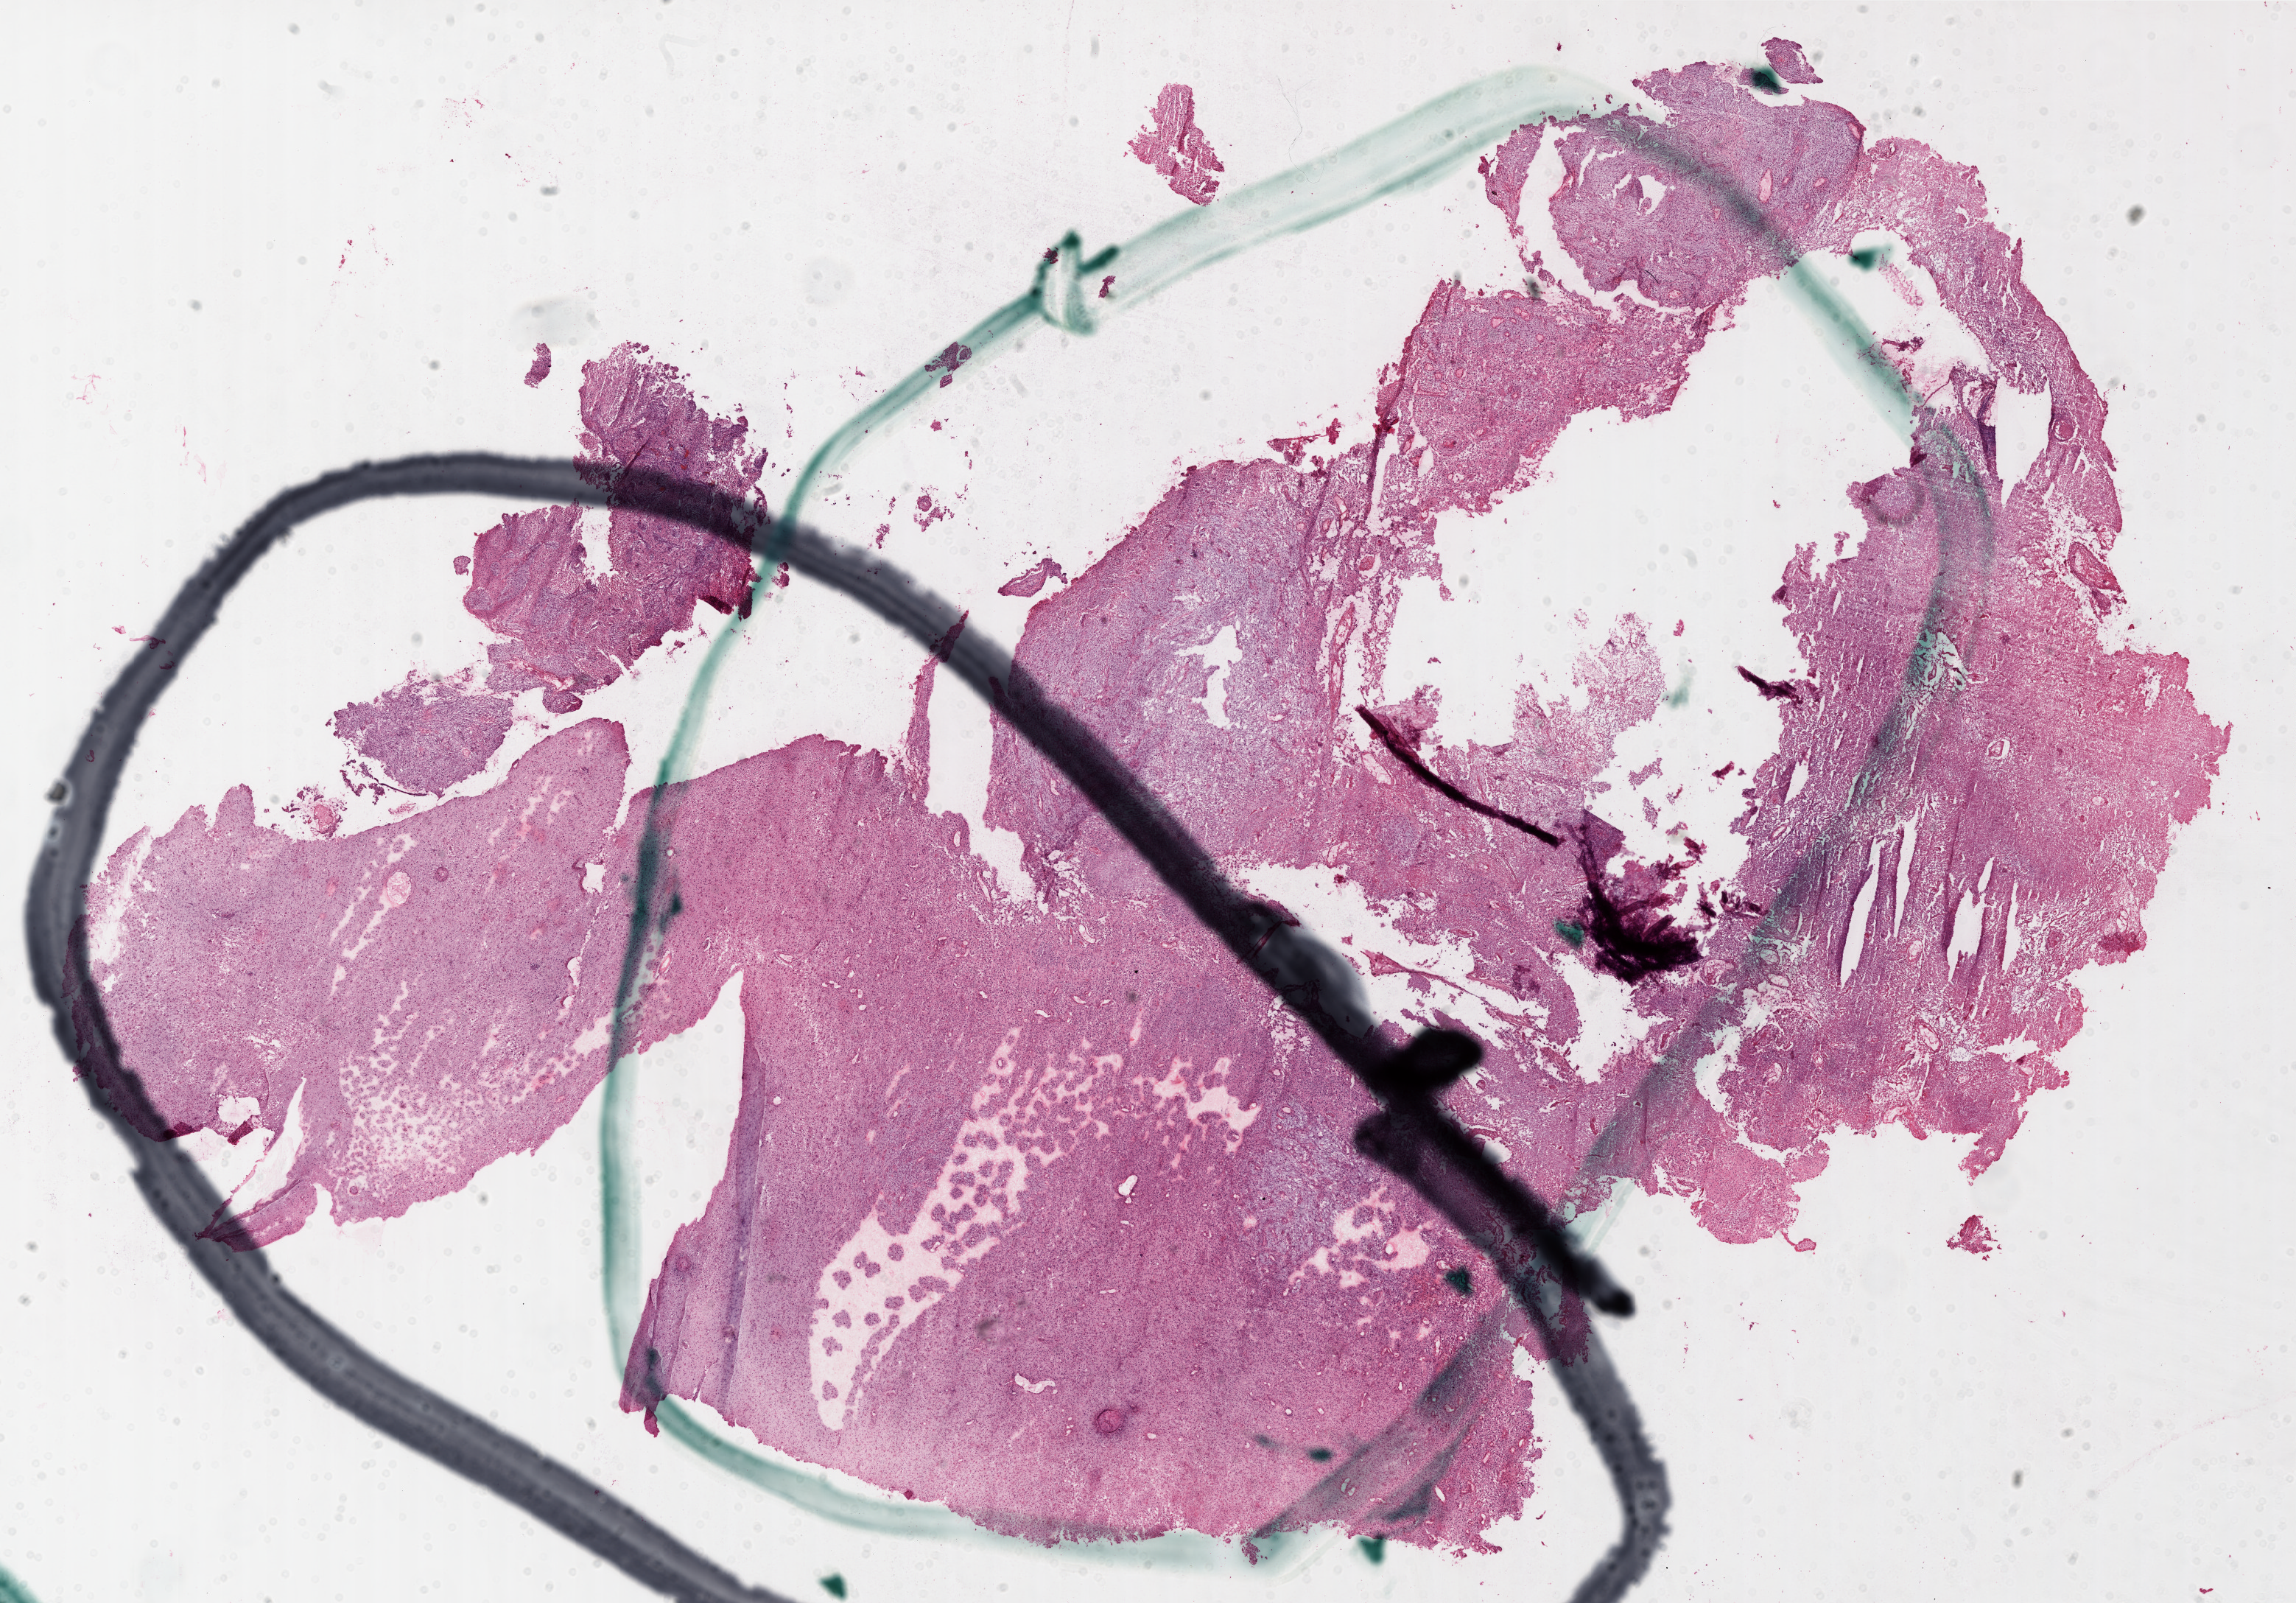
Digitized Hematoxylin and eosin (H&E) stained tissue section (whole slide), low-resolution overview of the scanned area, about 25.1 x 17.5 mm. Formalin-fixed paraffin-embedded (FFPE) diagnostic section. Sample: primary tumour, brain. Female, age 63 years at initial diagnosis.
- pathologic diagnosis: Glioblastoma